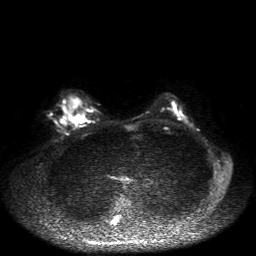
Breast MRI, one axial slice. Position 29 of 50 along the scan axis. Diffusion-weighted series; image 2 of 4 stored at this slice position (different b-values; order by instance number). 1.5 T. 256 × 256 image matrix, field of view 360 × 360 mm. Female patient.
Annotated regions visible in this slice (manually delineated by an expert):
- tumour on diffusion-weighted imaging: bounding box [x1, y1, x2, y2] px = [75, 114, 84, 123]